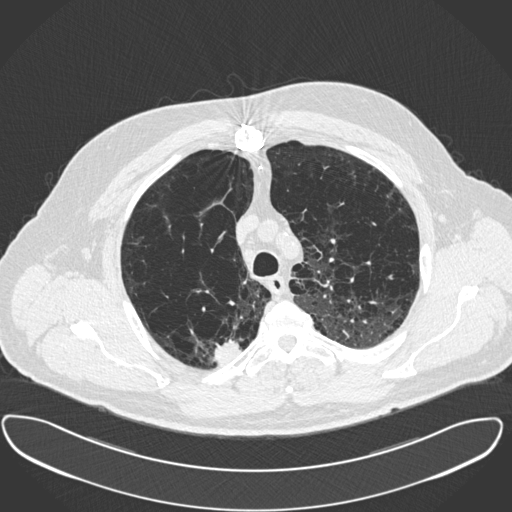
Low-dose screening chest CT, one axial slice; position 303 of 385 along the scan axis; reconstruction kernel B30f; 120 kVp; lung window (W 1500 / L -600 HU); 1 mm slice thickness; 512 × 512 image matrix, field of view 408 × 408 mm.
Annotated regions visible in this slice (outlined manually by an expert reader):
- lesion 1 (tumor, upper lobe of right lung): bounding box <212,339,241,364> (left, top, right, bottom; pixels)